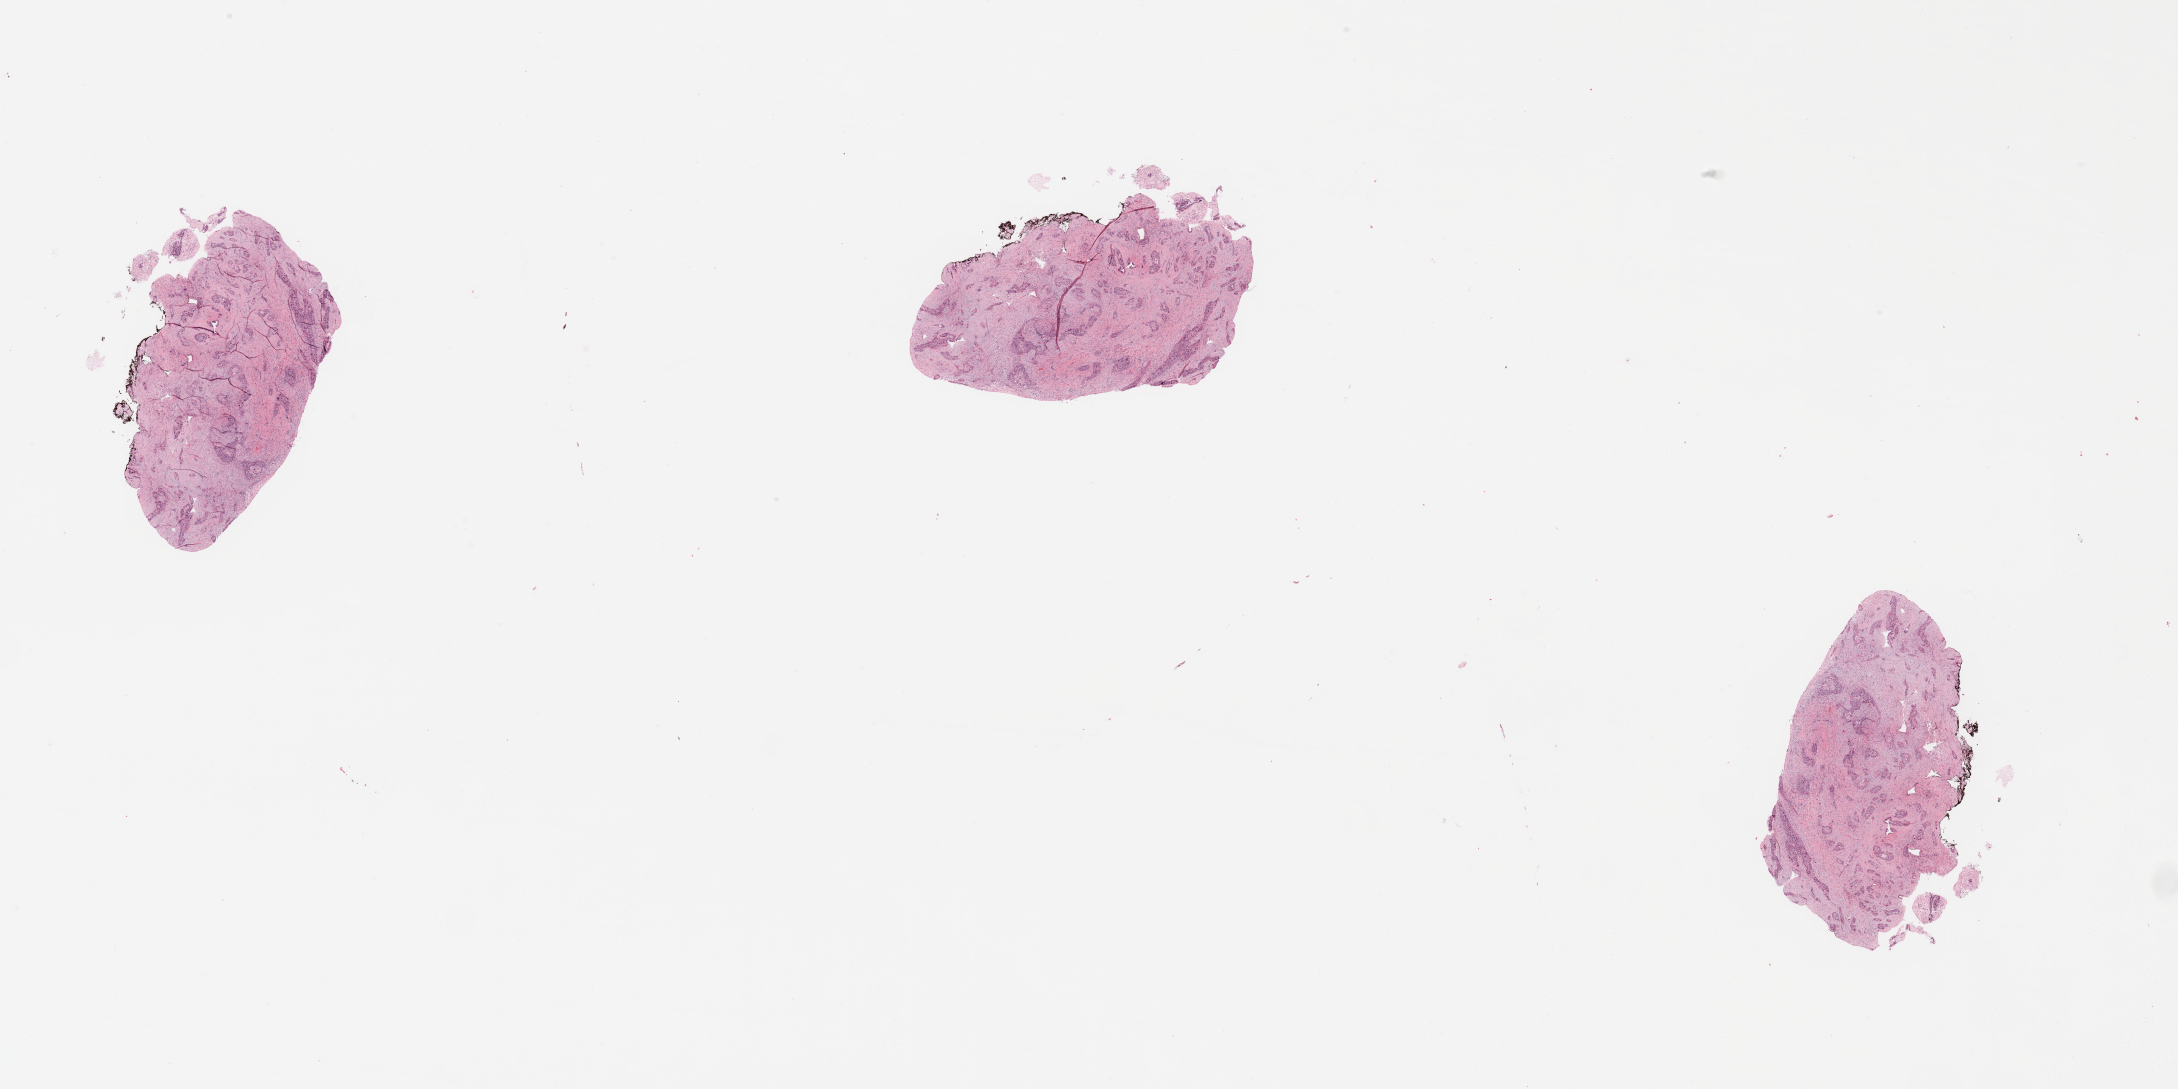
H&E-stained whole-slide image — low-resolution overview of the scanned area, about 34.5 x 17.2 mm (from a 20x scan), tumour tissue sample, sampled site: pancreas. Female, 68 y/o. Histologic grade: G2 (moderately differentiated). Pathologist review of this section (percent, as recorded): tumour nuclei 50%, necrosis 1%.
• primary tumour site (as recorded): head
• diagnosis: Infiltrating duct carcinoma, NOS
• AJCC pathologic stage: IIB